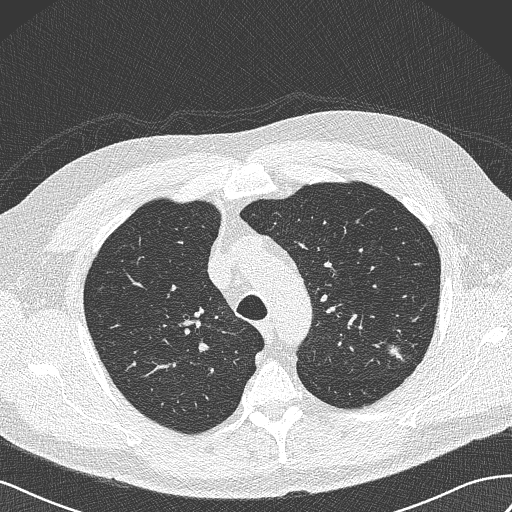
Low-dose screening chest CT, axial slice. Baseline annual screen. Lung window (W 1500 / L -600 HU). 120 kVp. Slice 107 of 462 in the series. Male, age 65 years at enrolment.
• Expert reader's lesion annotation, bounding box <383,341,417,372> (left, top, right, bottom; pixels).
• The screening reader recorded 3 non-calcified nodules or masses ≥4 mm on this exam (left upper lobe, left upper lobe, right upper lobe); which of them this box marks is not recorded.
• Official screen result: positive, change unspecified: nodule(s) >= 4 mm or enlarging nodule(s), mass(es), or other non-specific abnormalities suspicious for lung cancer.
• Lung cancer was diagnosed 541 days after this screen (after the second annual screen): adenocarcinoma, NOS, left upper lobe, poorly differentiated (G3), stage IA (AJCC 6th edition), 13 mm at pathology.